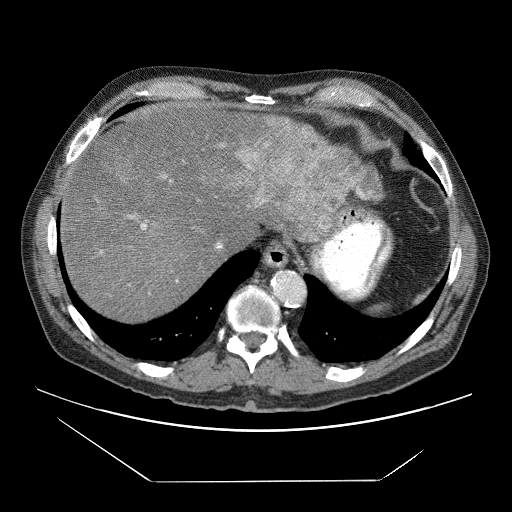
Contrast-enhanced abdominal CT (liver protocol), one axial slice; position 59 of 83 along the scan axis; reconstruction kernel STANDARD; soft-tissue window (W 400 / L 40 HU); 2.5 mm slice thickness; 512 × 512 image matrix. From the clinical record (not read from this slice): diagnosis: hepatocellular carcinoma (patient treated with transarterial chemoembolisation; whether this scan precedes or follows treatment is not stated here); TNM stage (as recorded): Stage-IVB; Child-Pugh class: B; tumour differentiation: poorly differentiated; tumour nodularity: uninodular.
Annotated regions visible in this slice (semi-automatically segmented with operator editing):
- liver parenchyma outside the tumour (the mass and vessels are separate outlines, so this box may not span the whole liver): bounding box <60,104,380,320> (left, top, right, bottom; pixels)
- mass: <237,116,380,239>
- liver vessels: <100,144,372,286>